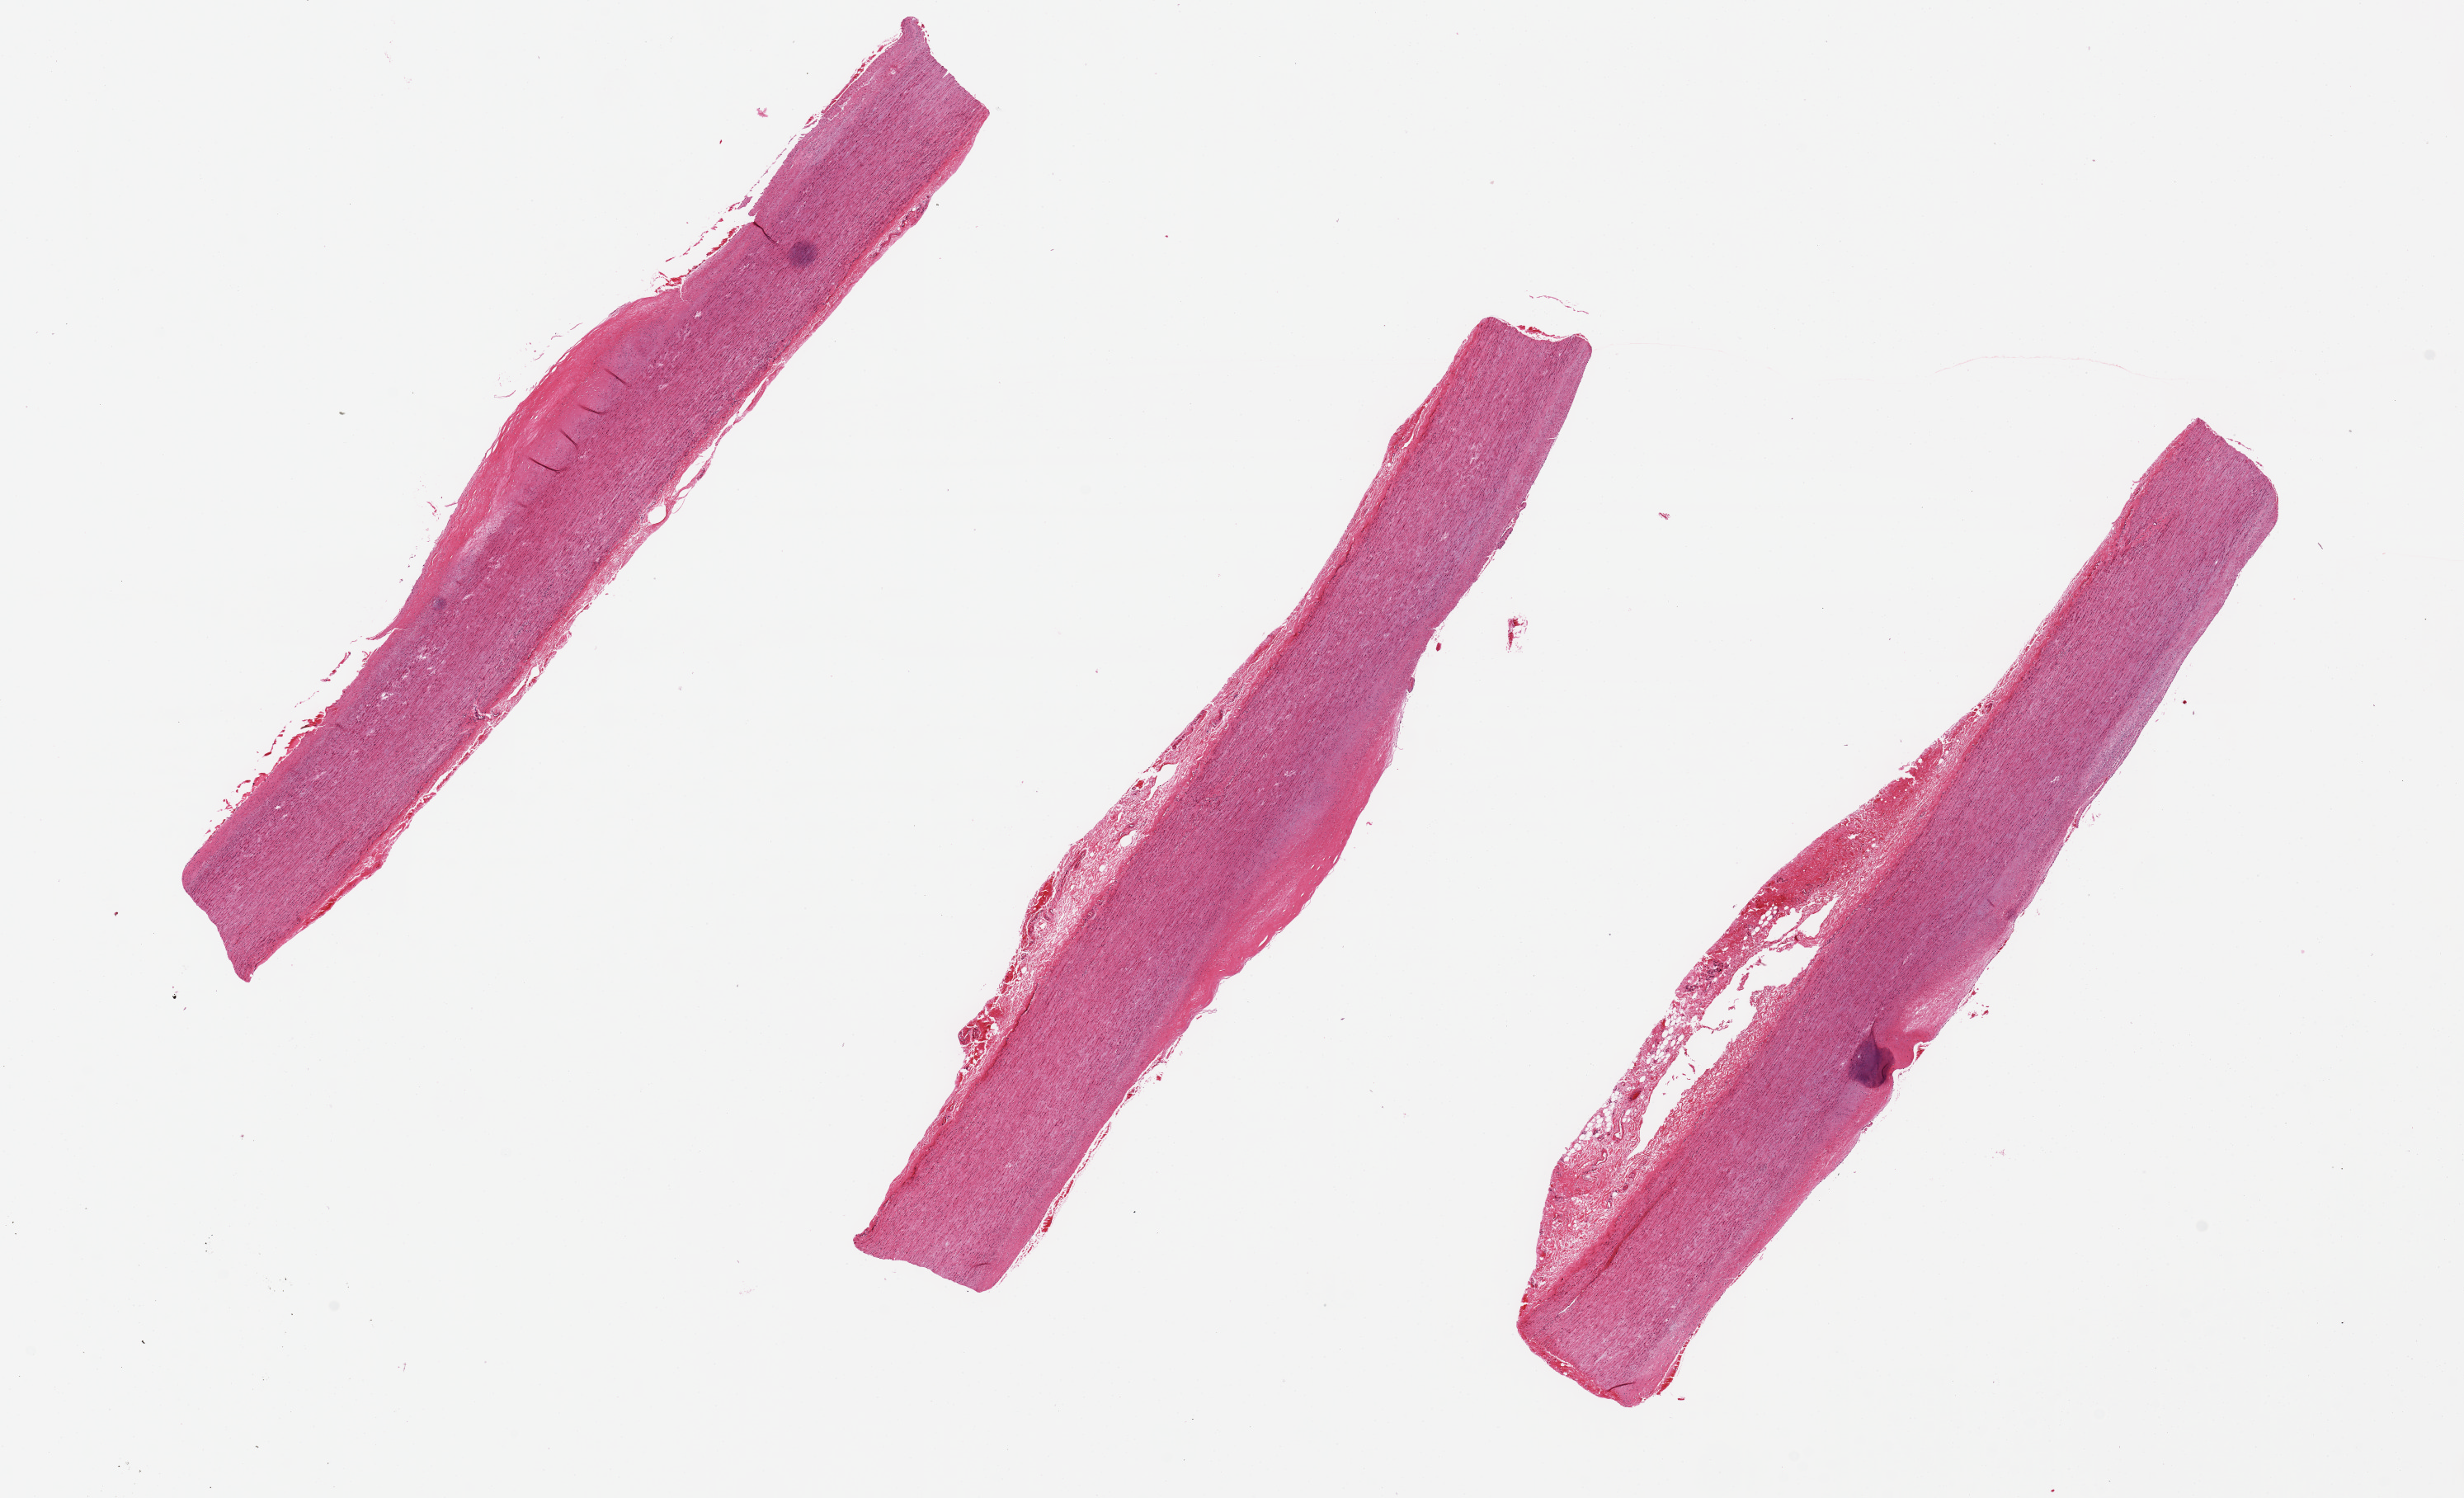
Whole-slide image, hematoxylin and eosin (H&E) stain, brightfield — low-resolution overview of the scanned area, about 23.6 x 14.4 mm; PAXgene-fixed, paraffin-embedded tissue; section of aorta (target tissue); tissue donor sample. Donor sex: female.
Reviewer comment on this tissue sample: Moderate atherosis.